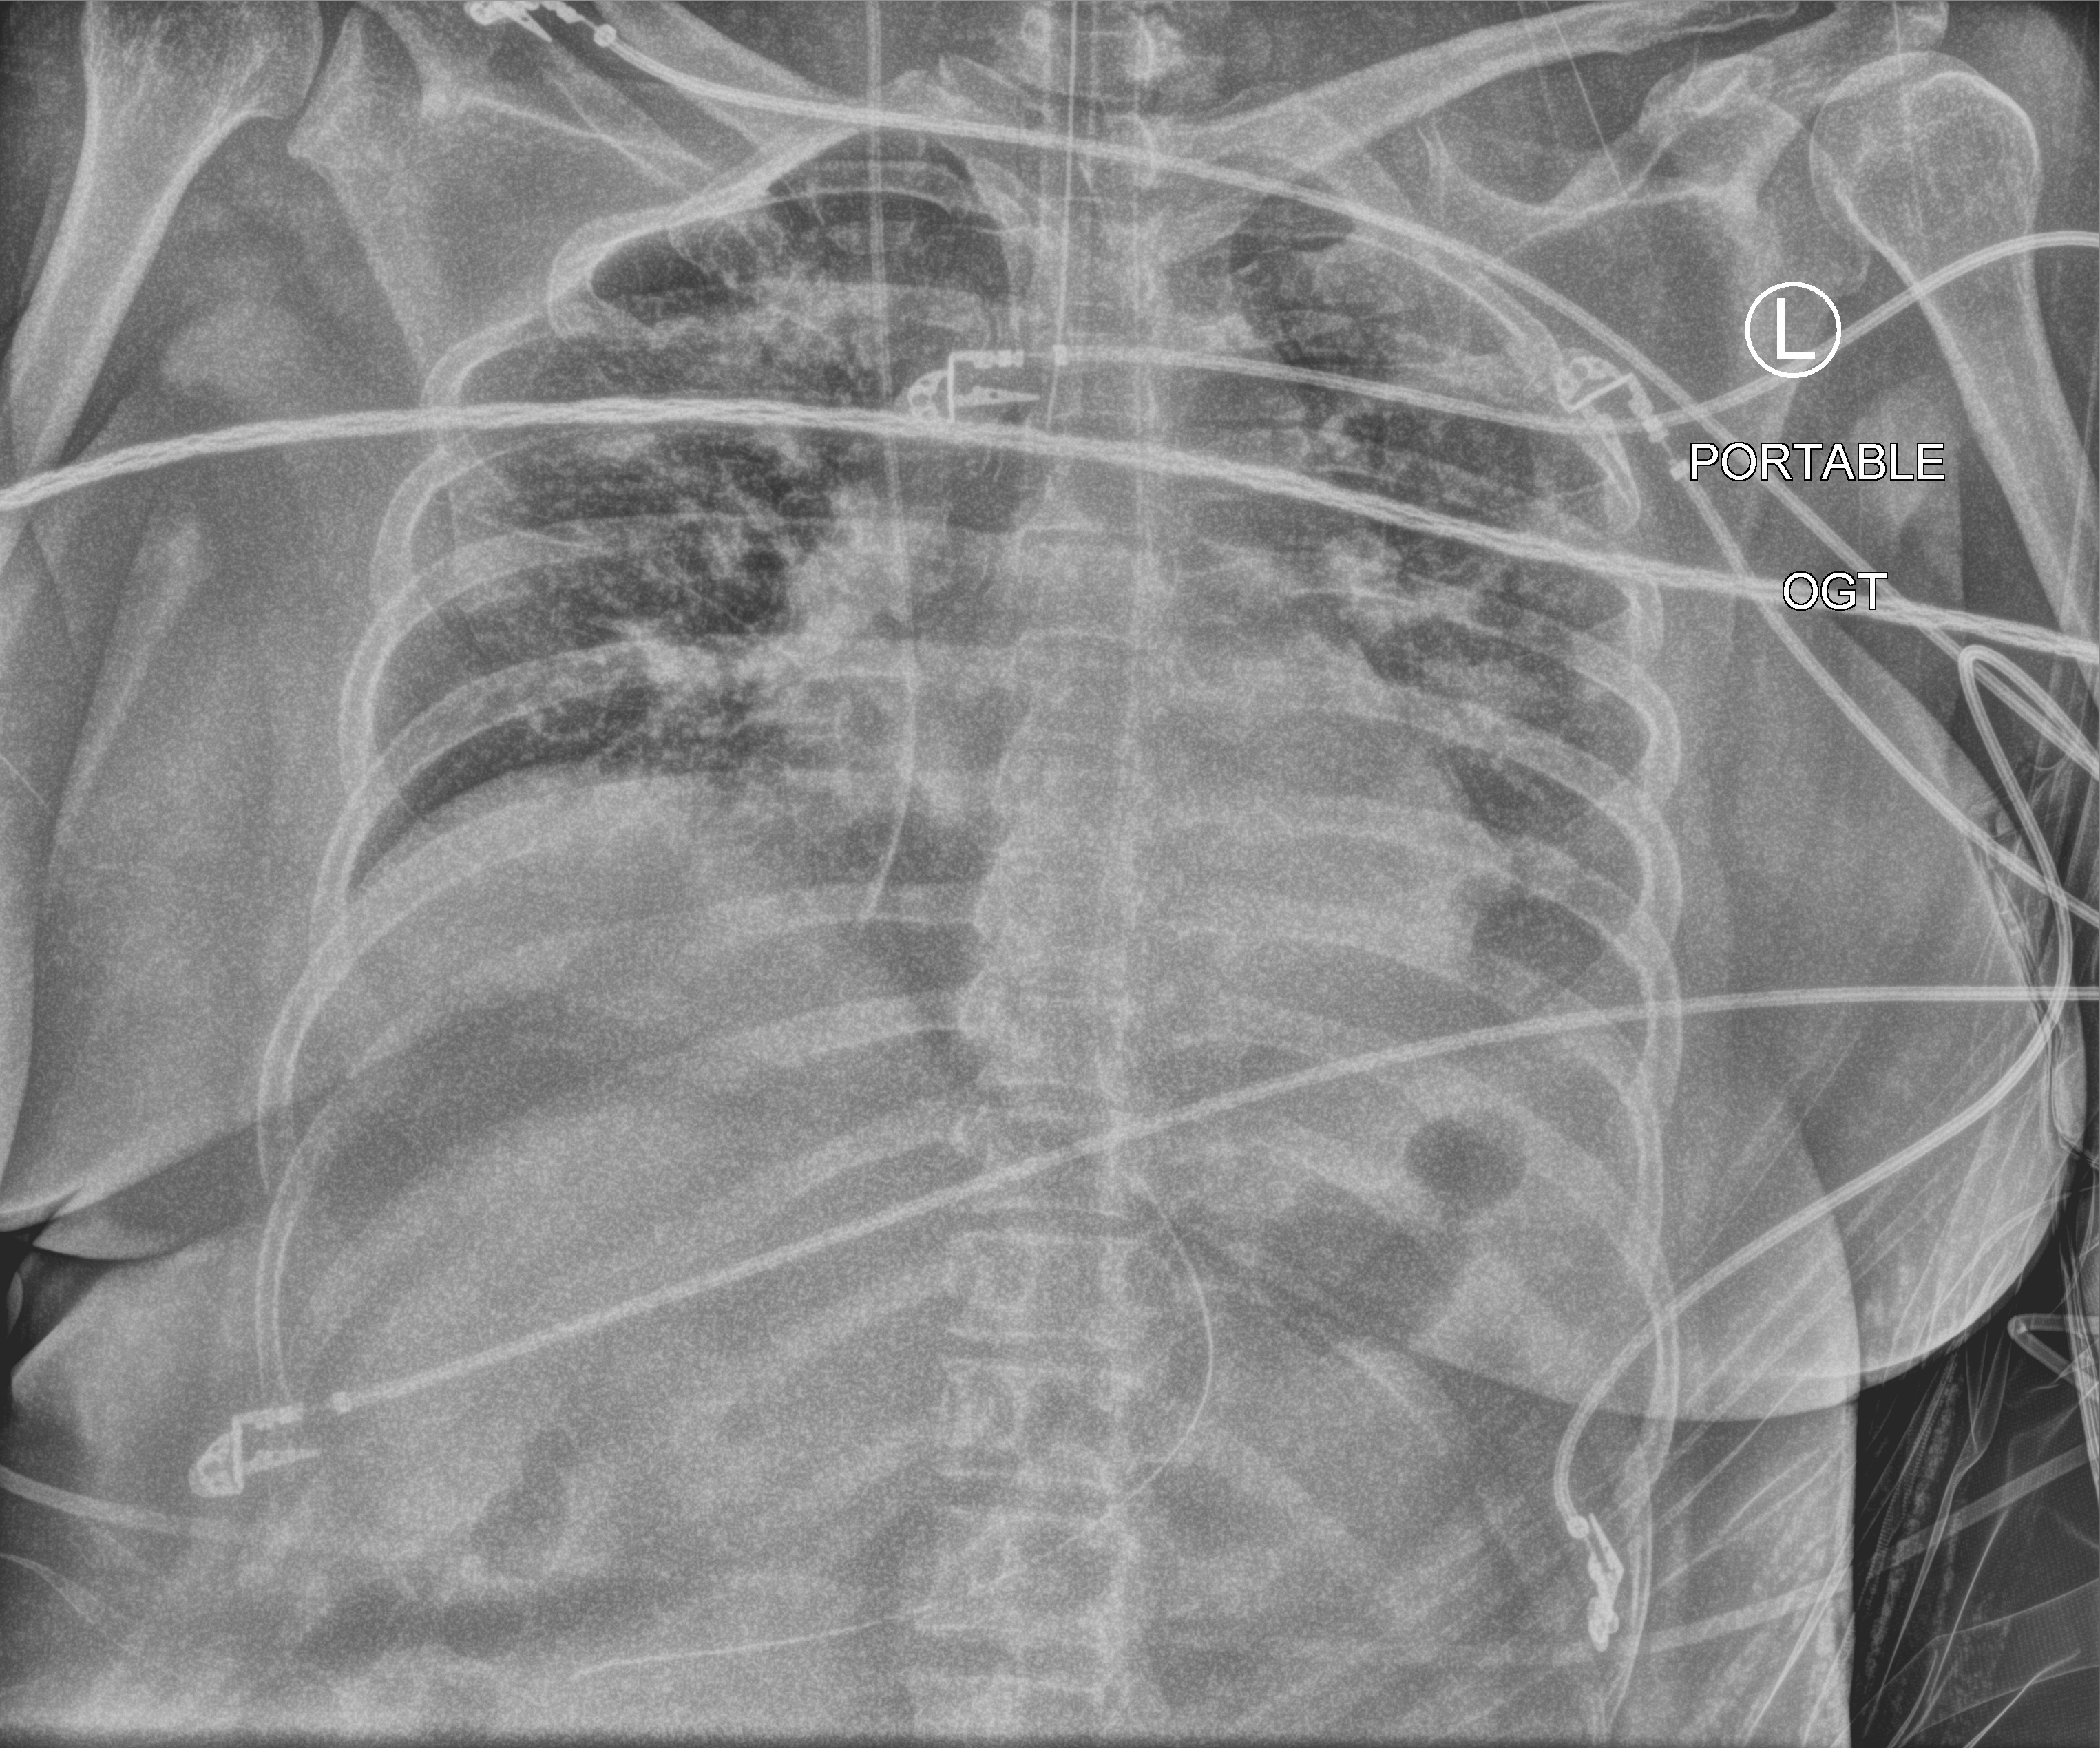
Chest X-ray (portable), anteroposterior (AP) projection. Female patient hospitalised with COVID-19, age 18–59 years.
Admission-level facts for this patient (not findings on this image; timing relative to this image not recorded):
- COPD (admission record): no
- mechanically ventilated during this hospital stay: yes
- admitted to intensive care during this hospital stay: yes